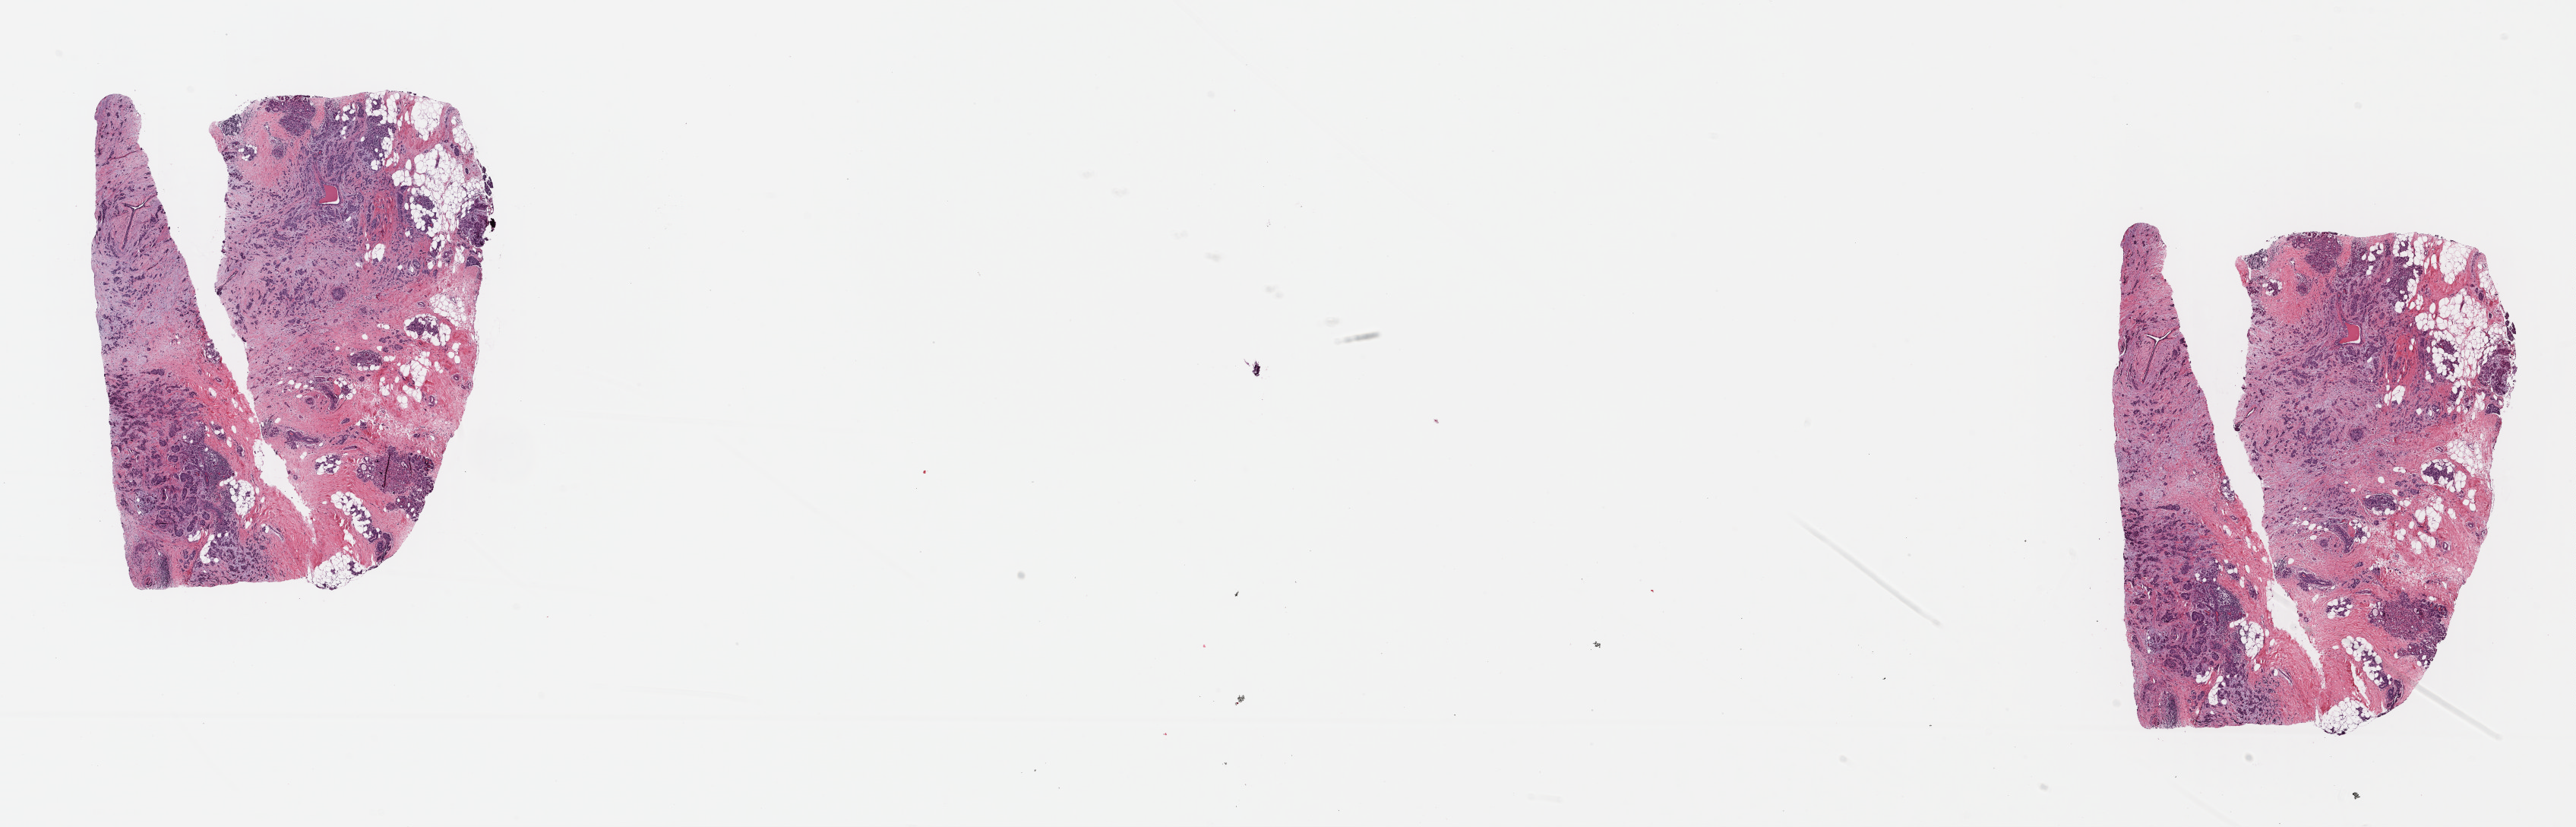
Whole-slide histology image, Hematoxylin and eosin (H&E) stained, whole scanned area (about 26.7 x 8.6 mm) shown as a low-resolution overview. FFPE section. Primary tumour sample from the breast. Female, age 37 years at initial diagnosis.
• AJCC pathologic stage: IIA
• histologic diagnosis: Infiltrating duct carcinoma, NOS
• laterality: left